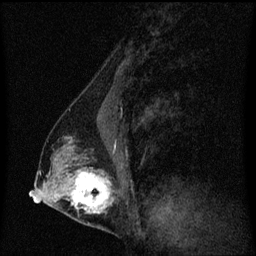
Breast MRI (dynamic contrast-enhanced), one sagittal slice. Slice 30 of 60 in the series (ordered by position). Dynamic contrast-enhanced series, image 2 of 3 at this slice position (ordered by acquisition). 1.5 T. TE 4.2 ms, TR 8.4 ms. 2 mm slice thickness. 256 × 256 image matrix, field of view 200 × 200 mm. Female patient, age 40 years. Case-level facts recorded for this patient, not image findings: setting: breast cancer imaged before/during neoadjuvant chemotherapy; receptor status: triple-negative.
Outlined on this slice (semi-automatic segmentation, software-assisted and operator-edited):
- analysis volume of interest (the breast-tissue region the enhancement analysis was run in; not a lesion): bounding box <44,128,118,221> (left, top, right, bottom; pixels)
- tumour enhancement mask (voxels above the 70 % enhancement threshold inside the analysis volume of interest): <71,172,113,215>